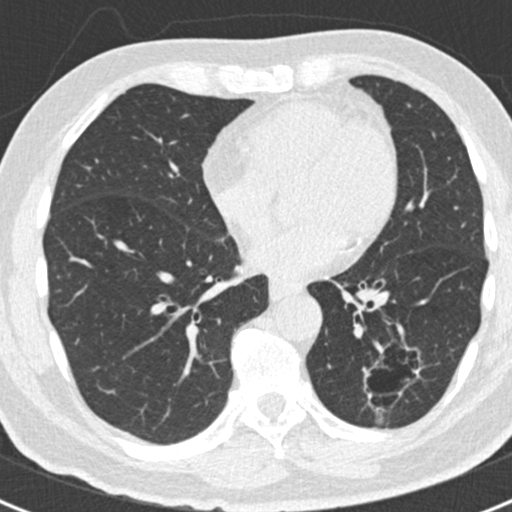
Axial slice from a low-dose chest CT screening exam; baseline screening round; lung window (W 1500 / L -600 HU); slice 101 of 188 in the series. Male, age 66 years at enrolment.
Expert-annotated lung lesion, bounding box (x1, y1, x2, y2) in pixels: (343, 338, 420, 416). The exam's reader record, not a measurement of the box and not confirmed to be the same lesion: non-calcified nodule or mass ≥4 mm, left lower lobe, 43 × 27 mm, smooth margins. Official screen result: positive, change unspecified: nodule(s) >= 4 mm or enlarging nodule(s), mass(es), or other non-specific abnormalities suspicious for lung cancer. Later outcome: lung cancer diagnosed 801 days after this screen — adenocarcinoma, NOS, left lower lobe, poorly differentiated (G3), stage IB (AJCC 6th edition), 38 mm at pathology.